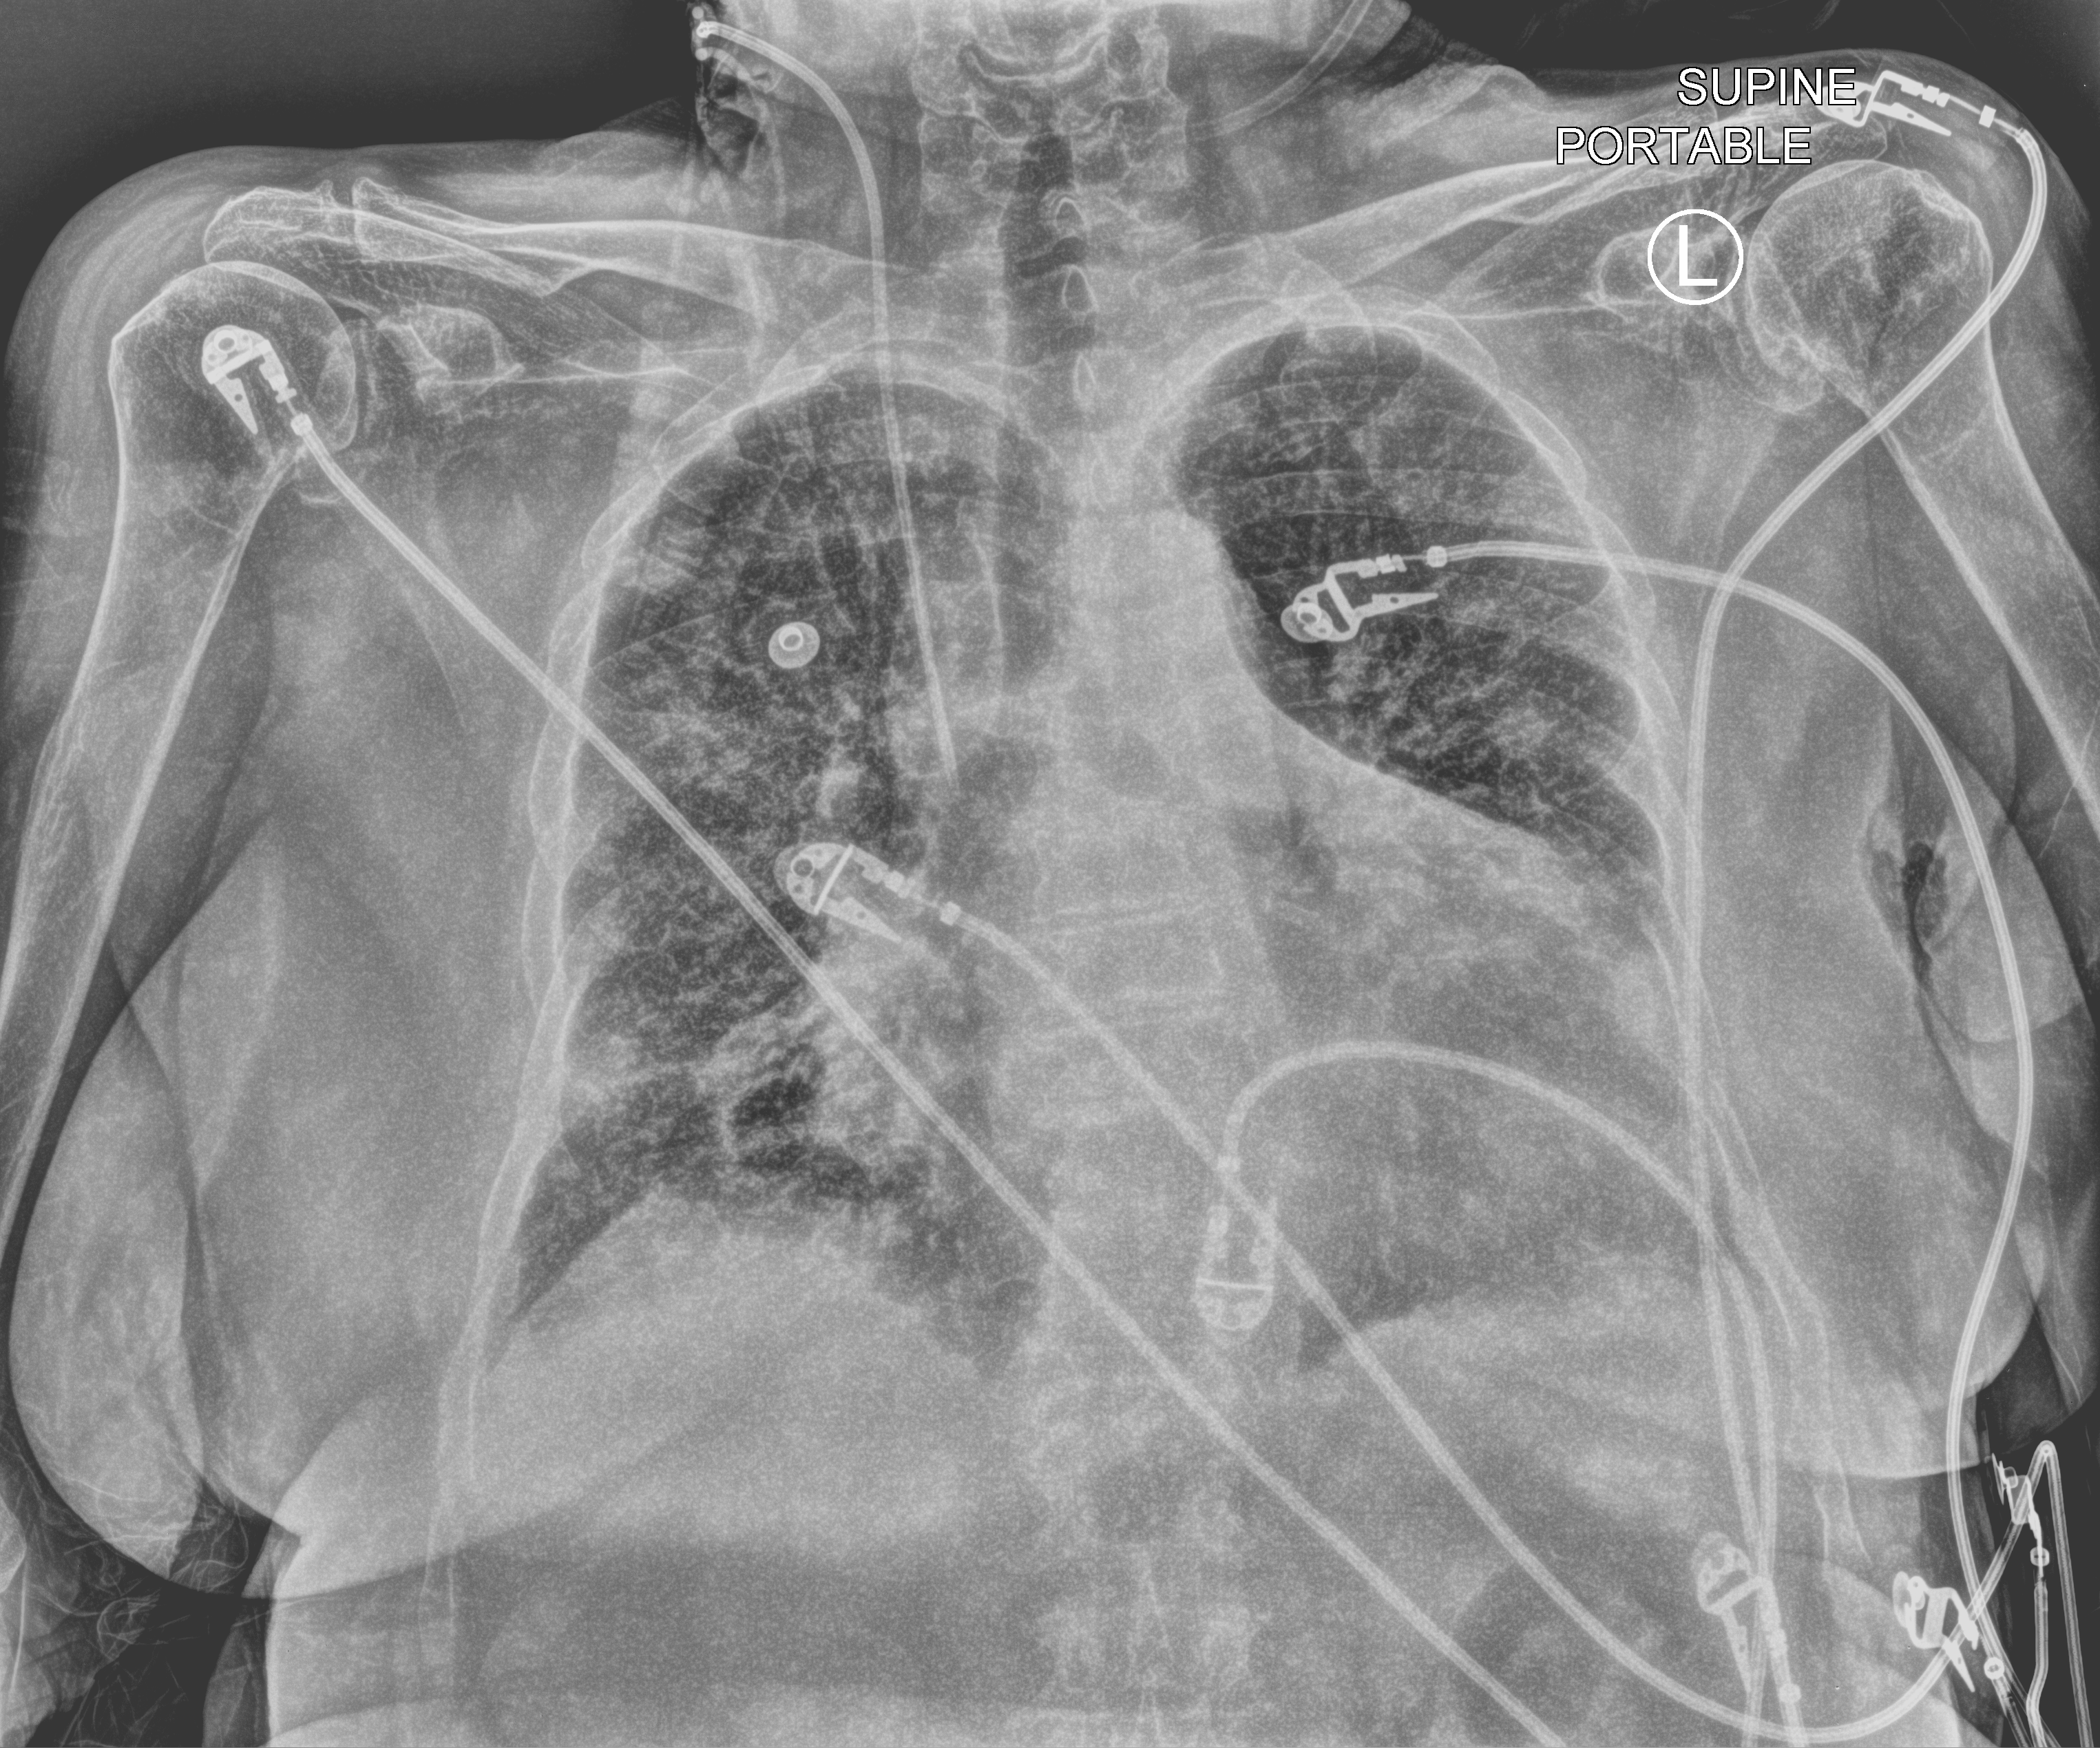
Portable chest radiograph, anteroposterior (AP) projection. Patient hospitalised with COVID-19; female, aged 75–90 years.
From the hospital-stay record, not from the radiograph (when in the stay this image was taken is not recorded): admitted to intensive care during this hospital stay: no; mechanically ventilated during this hospital stay: no.